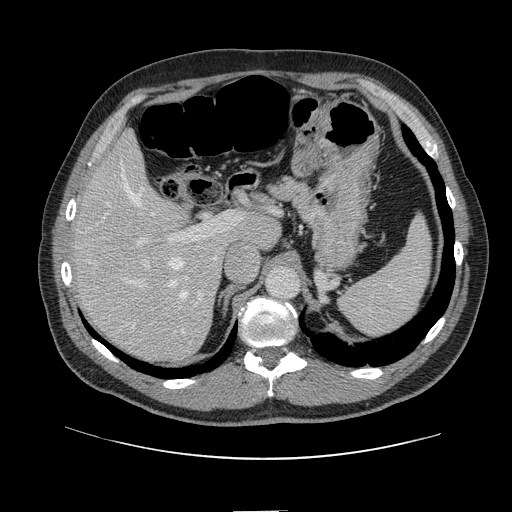
Contrast-enhanced abdominal CT, one axial slice; slice 90 of 161 in the series (ordered by position); 120 kVp; intravenous contrast given; soft-tissue window (W 400 / L 40 HU); 512 × 512 image matrix, field of view 412 × 412 mm. Male patient, age 66 years. Case-level facts recorded for this patient, not image findings: diagnosis: colorectal cancer liver metastases, imaged before liver resection; multiple liver metastases: no; largest metastasis: 3.5 cm; disease in both lobes: no.
Annotated regions visible in this slice (expert manual segmentation):
- hepatic veins: bounding box <103,164,188,329> (left, top, right, bottom; pixels)
- liver: <76,136,277,360>
- planned liver remnant (the part of the liver to remain after resection): <75,136,278,305>
- portal vein (with intrahepatic branches): <136,213,241,309>